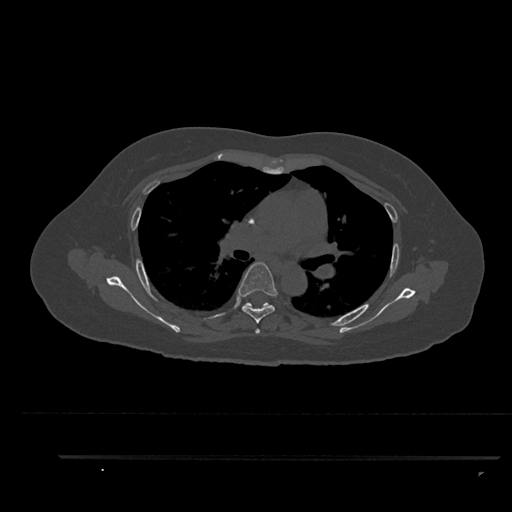
CT including the spine, one axial slice. Position 595 of 797 along the scan axis. Reconstruction kernel Br40s/3. 120 kVp. Bone window (W 1800 / L 400 HU). 0.5 mm slice thickness. 512 × 512 image matrix, field of view 408 × 408 mm. Patient: female, 44 years. Case-level facts recorded for this patient, not image findings: primary cancer: renal; vertebrae with lytic lesions (as recorded): L1.
Structures marked on this image (semi-automatically segmented with operator editing):
- T4 vertebra: box from (x=255, y=328) to (x=260, y=334) px
- T5 vertebra: (x=238, y=262)–(x=278, y=324)
- T6 vertebra: (x=242, y=302)–(x=270, y=309)